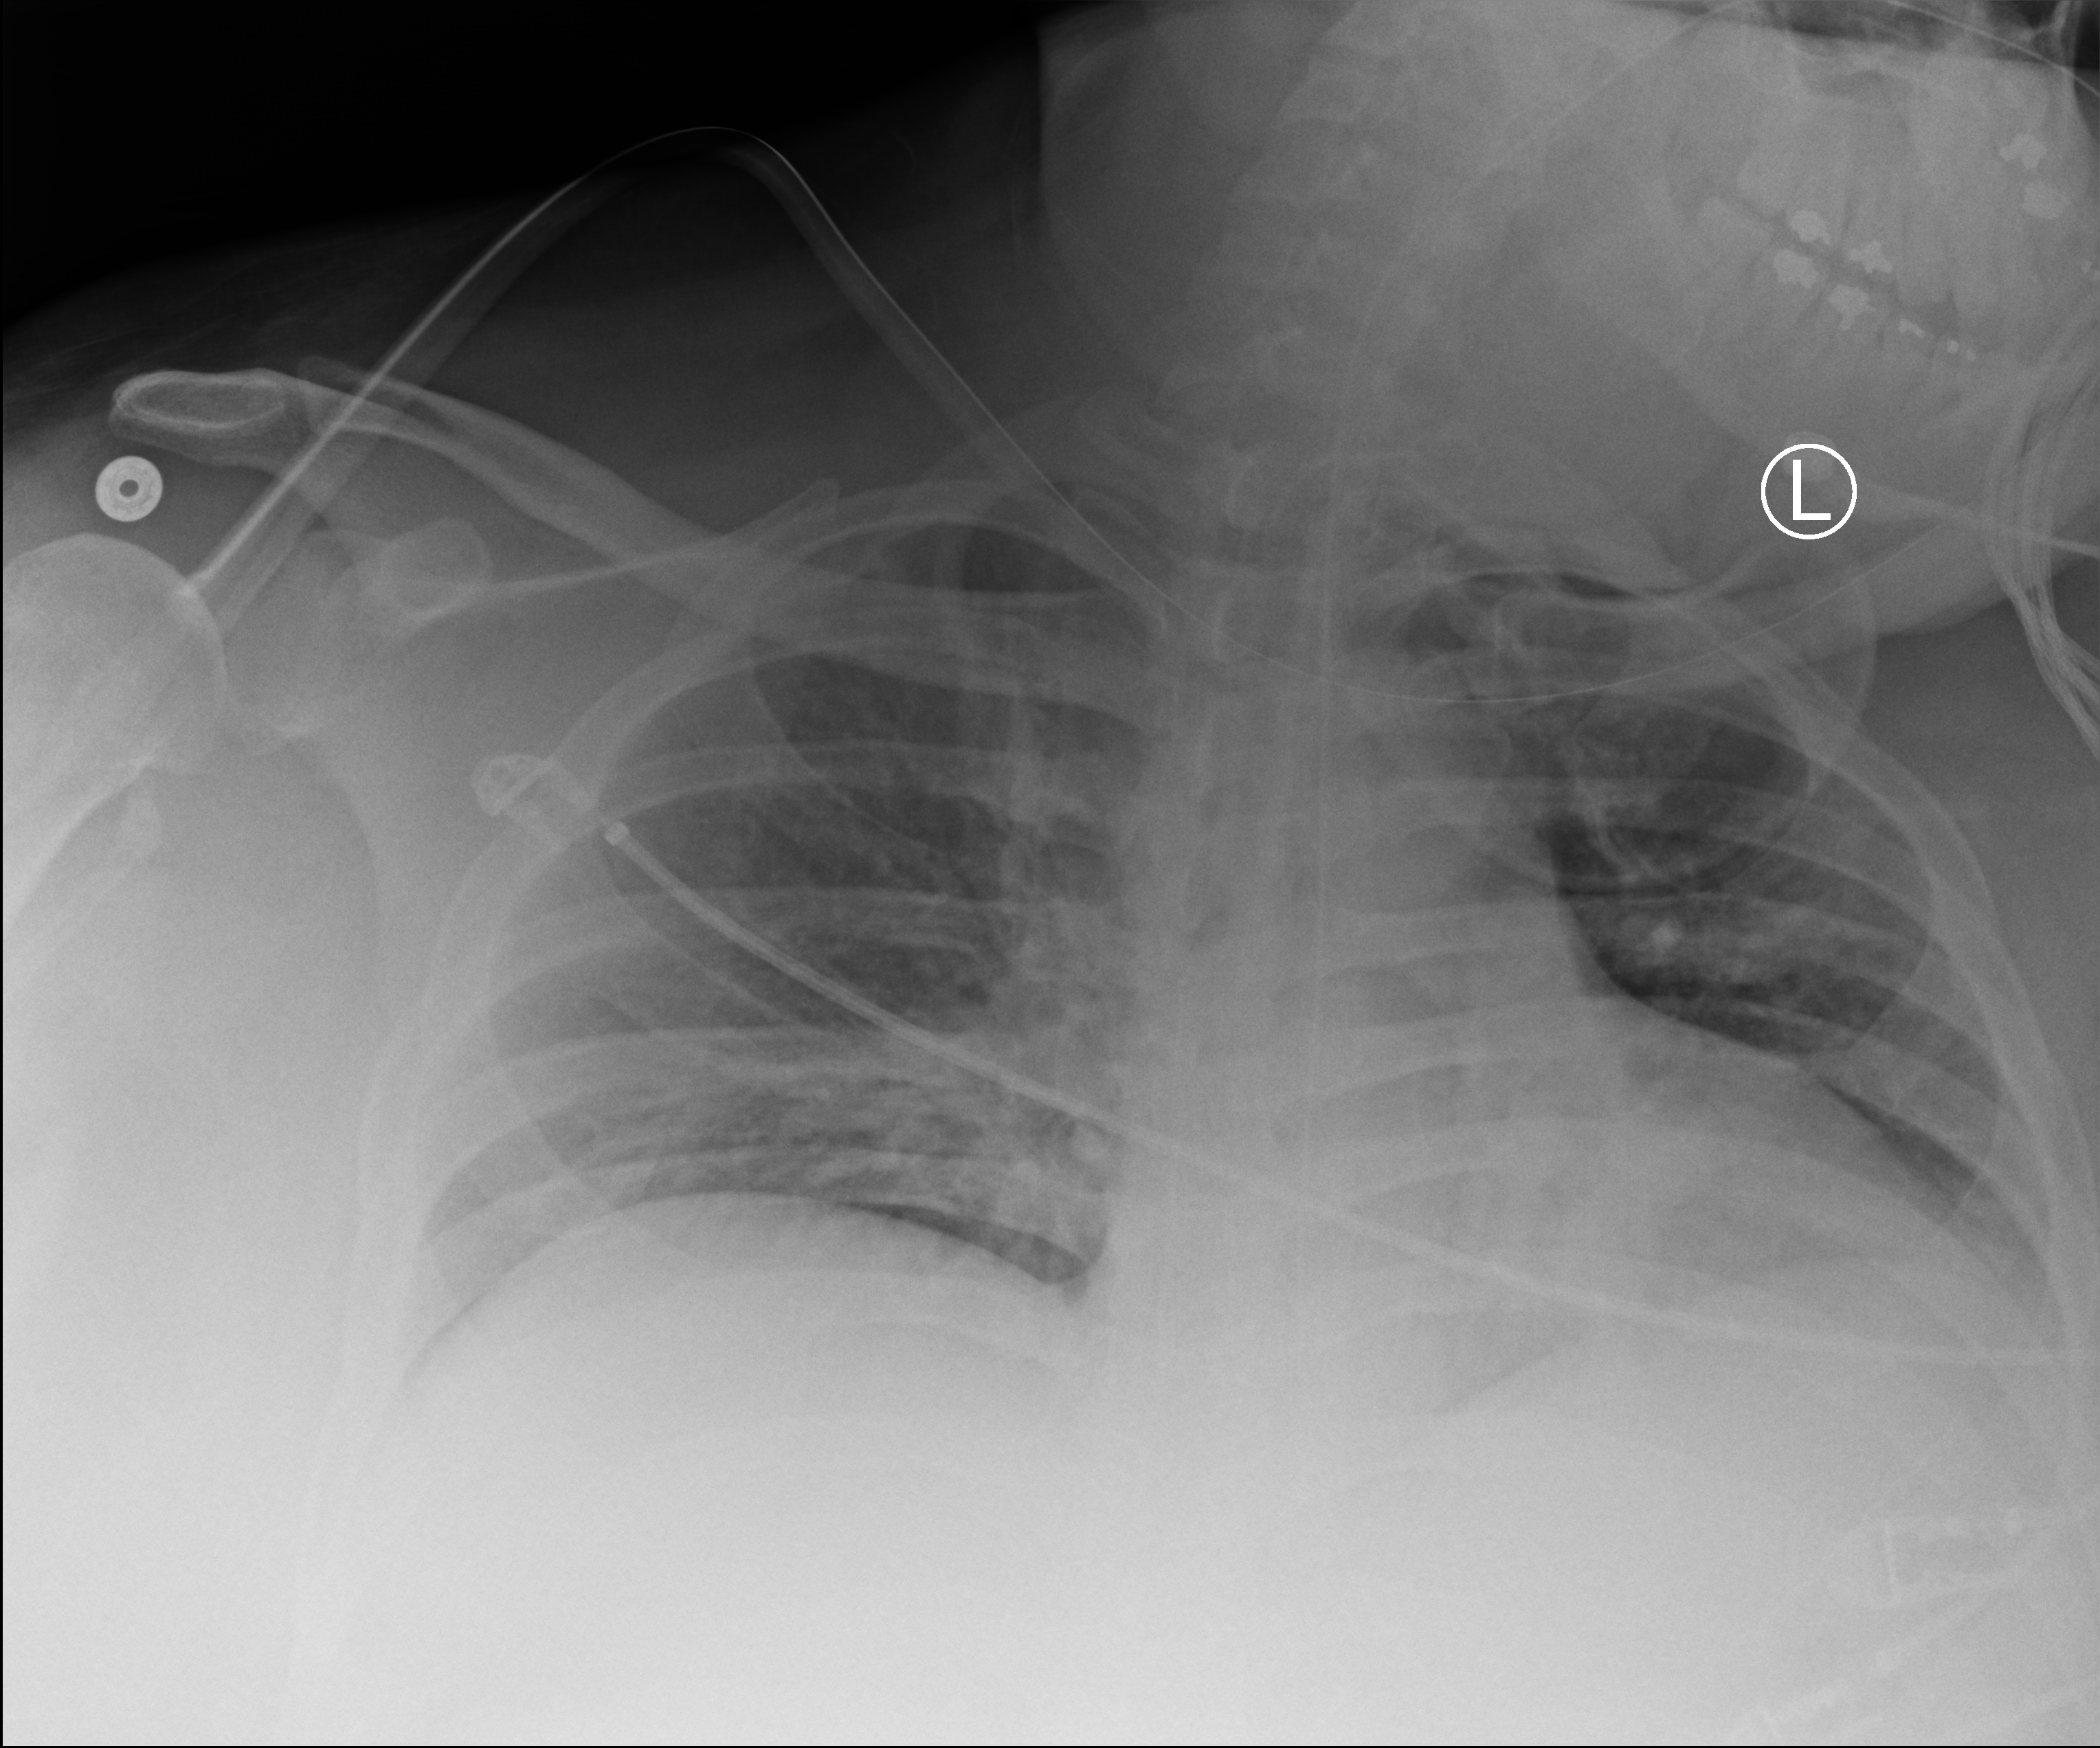
Bedside chest radiograph (computed radiography), anteroposterior (AP) projection. Patient hospitalised with COVID-19; male, aged 18–59 years.
Hospital-stay facts (about this admission, not read from this image; timing relative to this image not recorded): length of hospital stay: 69 days.